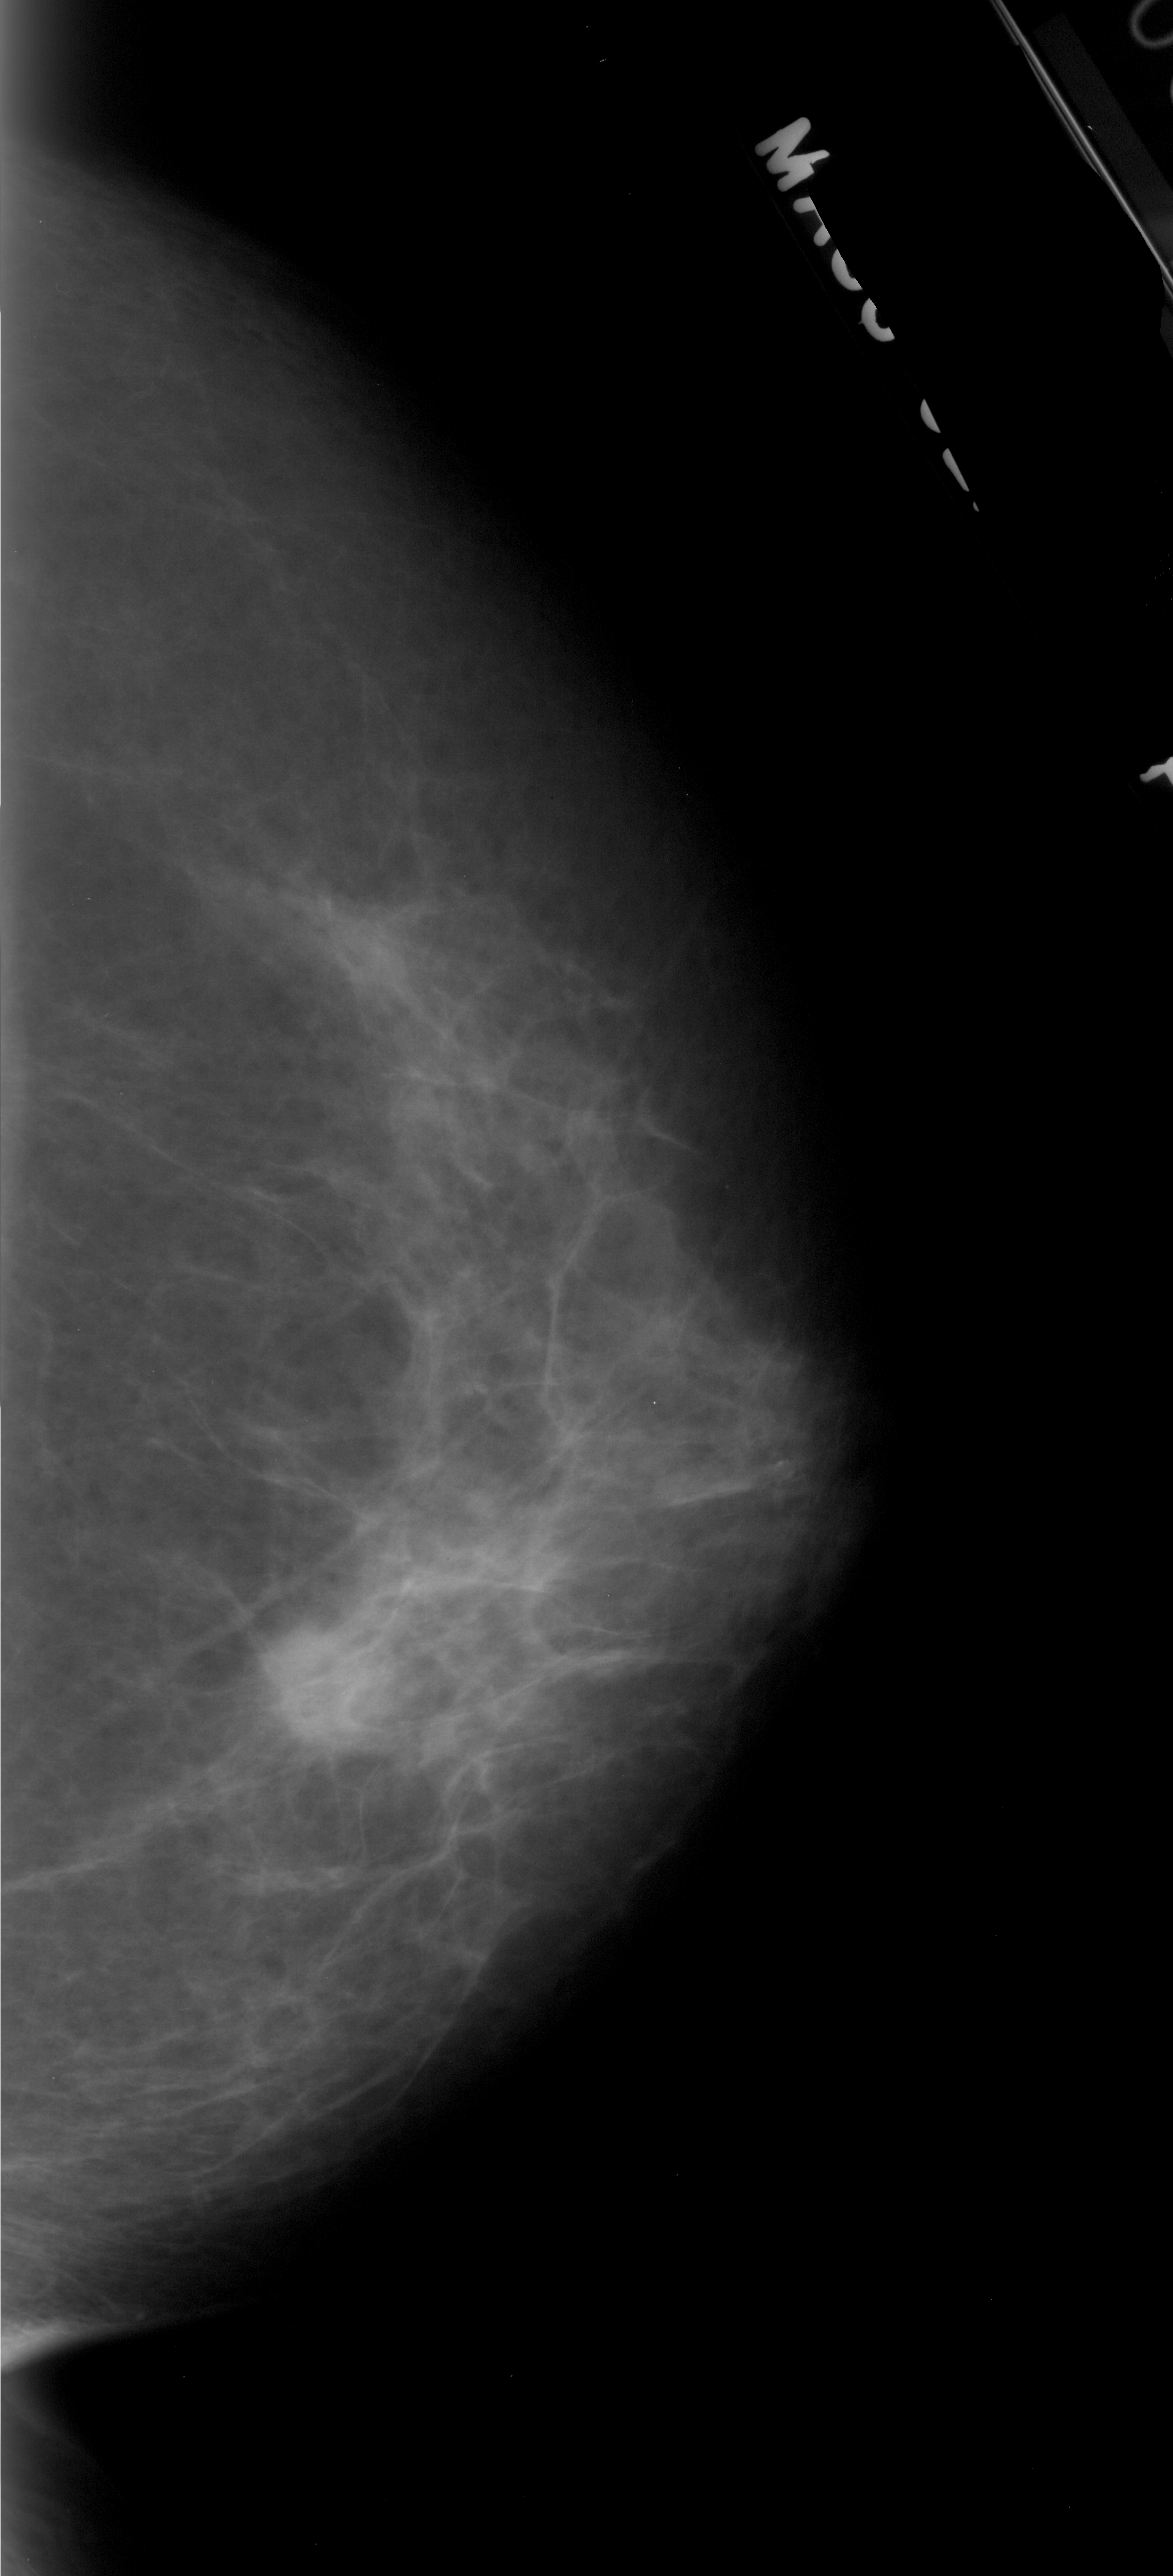
Scanned film-screen mammogram; right breast; craniocaudal (CC) view; BI-RADS breast density category 2 (scale 1–4).
Abnormality record for this image: mass, shape lobulated, margins ill defined; BI-RADS assessment category 4; pathology (as recorded): malignant.